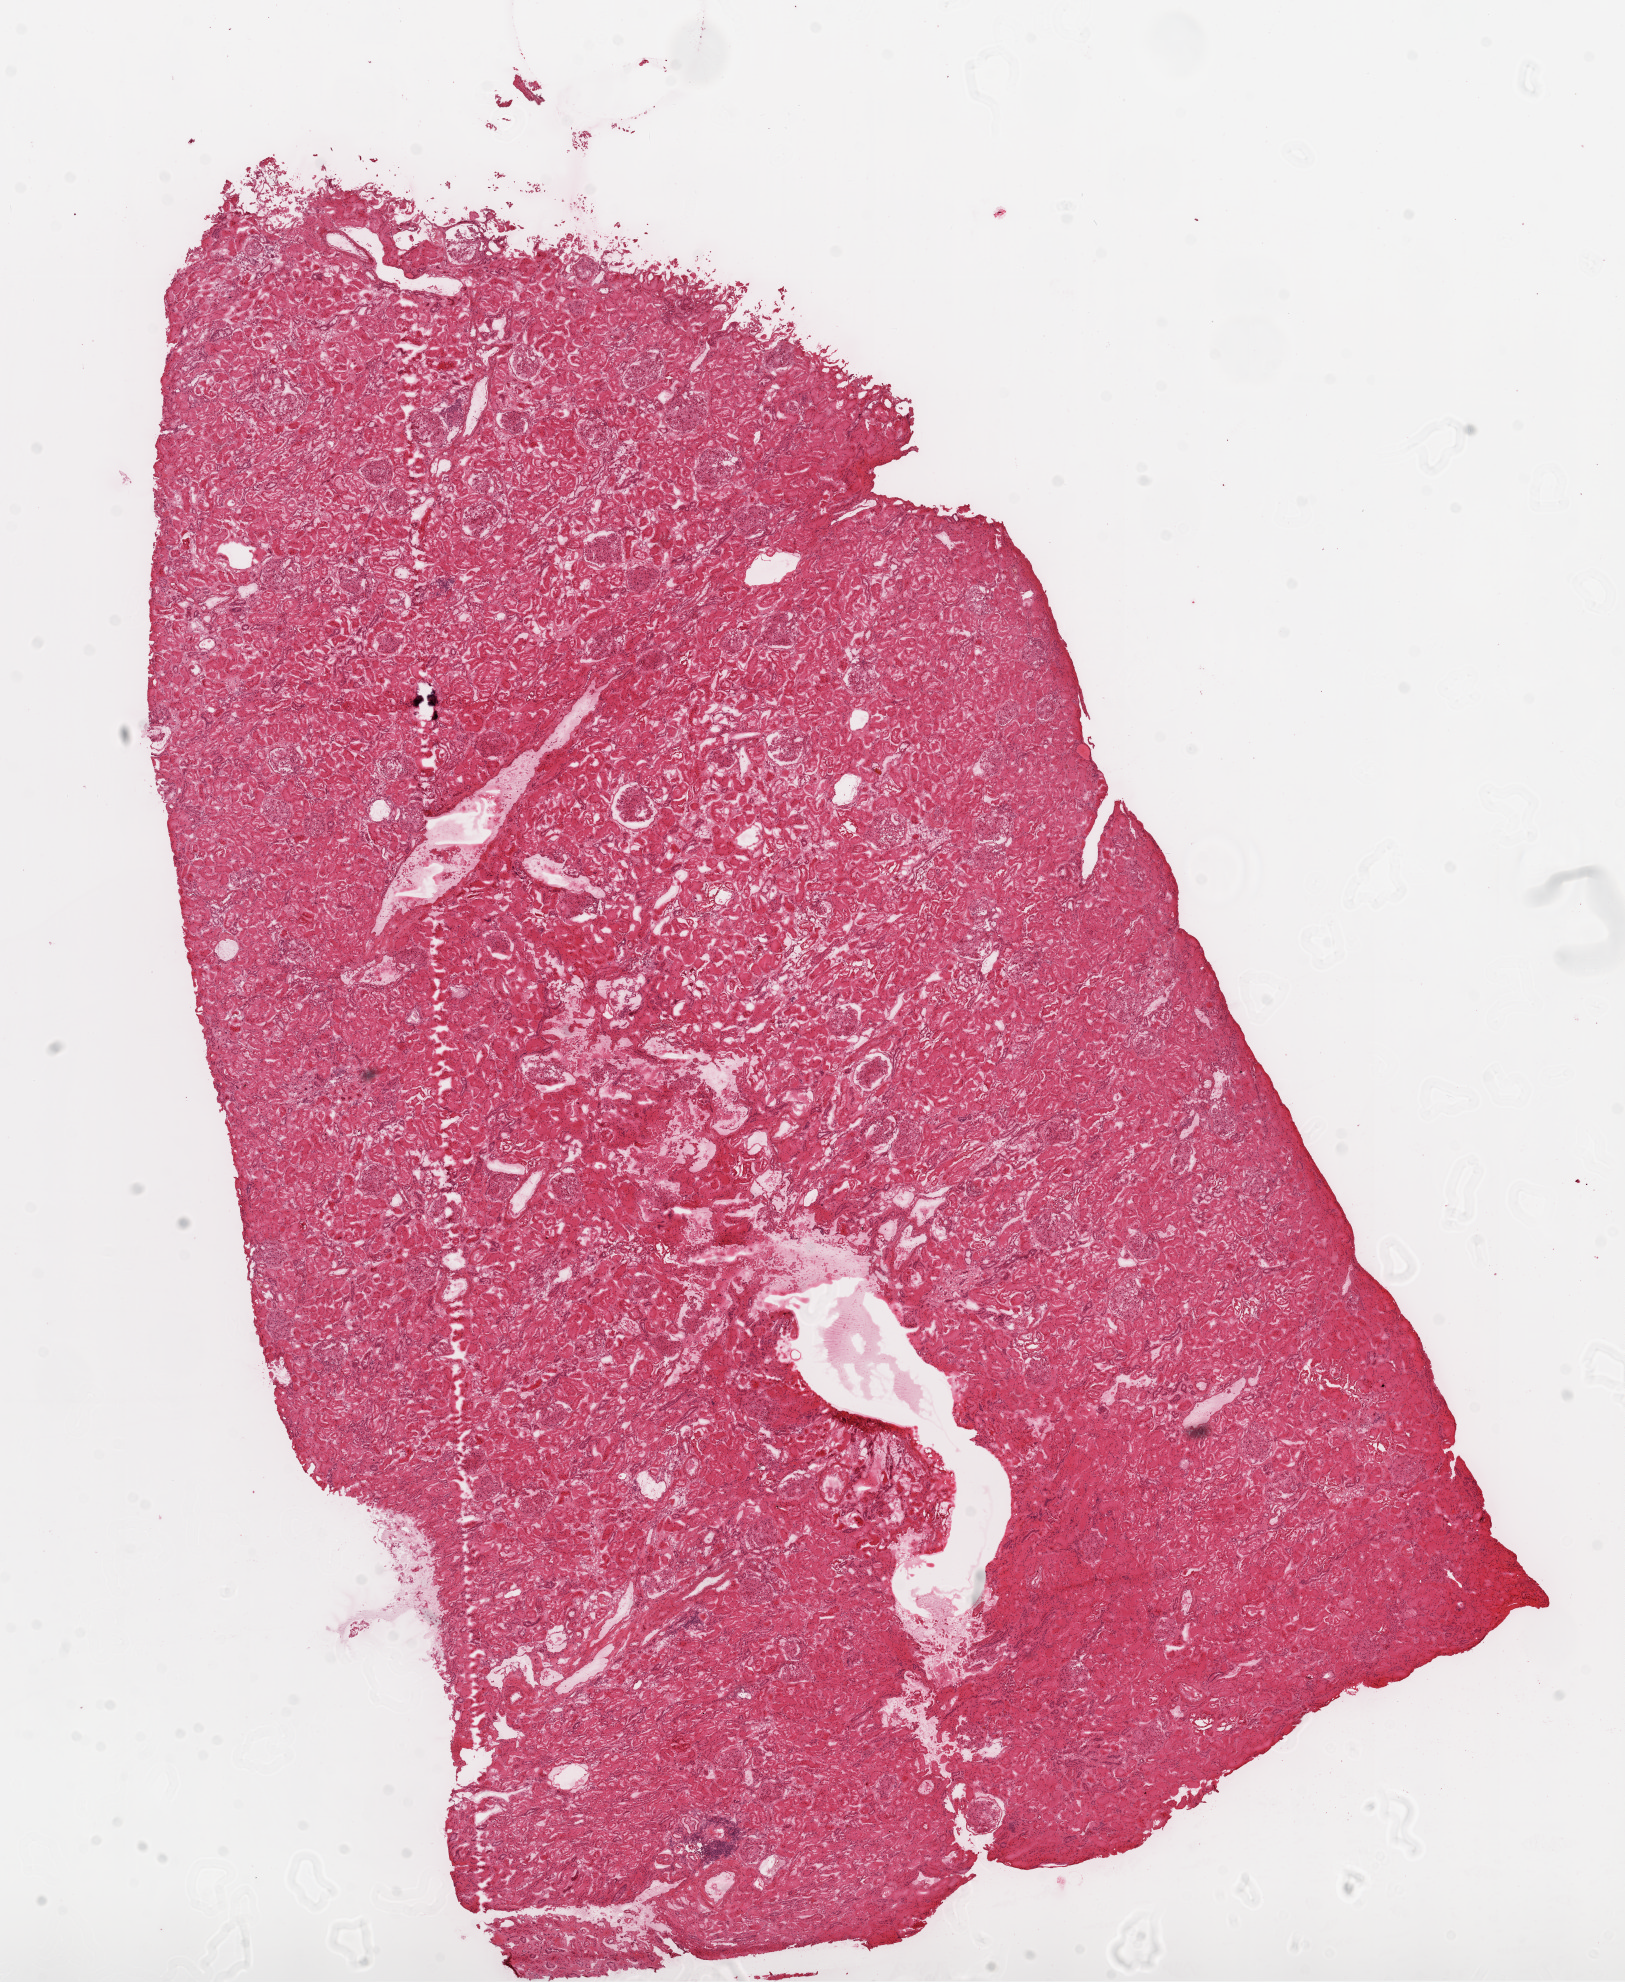
Whole-slide histology image, H&E — low-resolution overview of the scanned area, about 13.0 x 15.9 mm (from a 20x scan); frozen section; solid tissue normal (non-tumour tissue) sample from the kidney. Patient: male, age at initial diagnosis 66 years.
This section: solid tissue normal sample (biorepository sample class). Patient diagnosis: Clear cell adenocarcinoma, NOS.